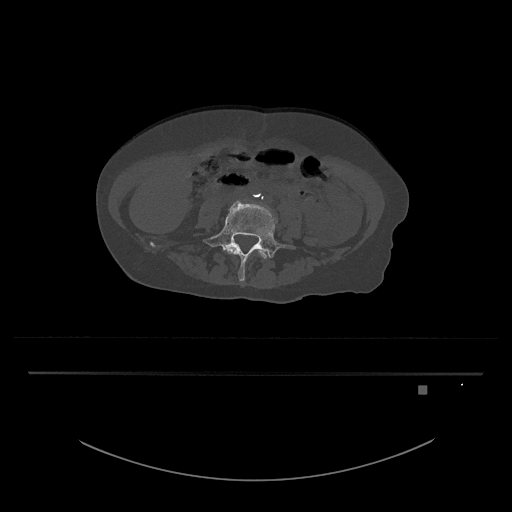
CT including the spine, one axial slice; position 317 of 797 along the scan axis; 120 kVp; bone window (W 1800 / L 400 HU); 512 × 512 image matrix, field of view 500 × 500 mm. Patient: female, 57 years. From the clinical record (not read from this slice): primary cancer: cervical.
Structures marked on this image (semi-automatically segmented with operator editing):
- L4 vertebra: bounding box (x1, y1, x2, y2) in pixels: (224, 244, 269, 259)